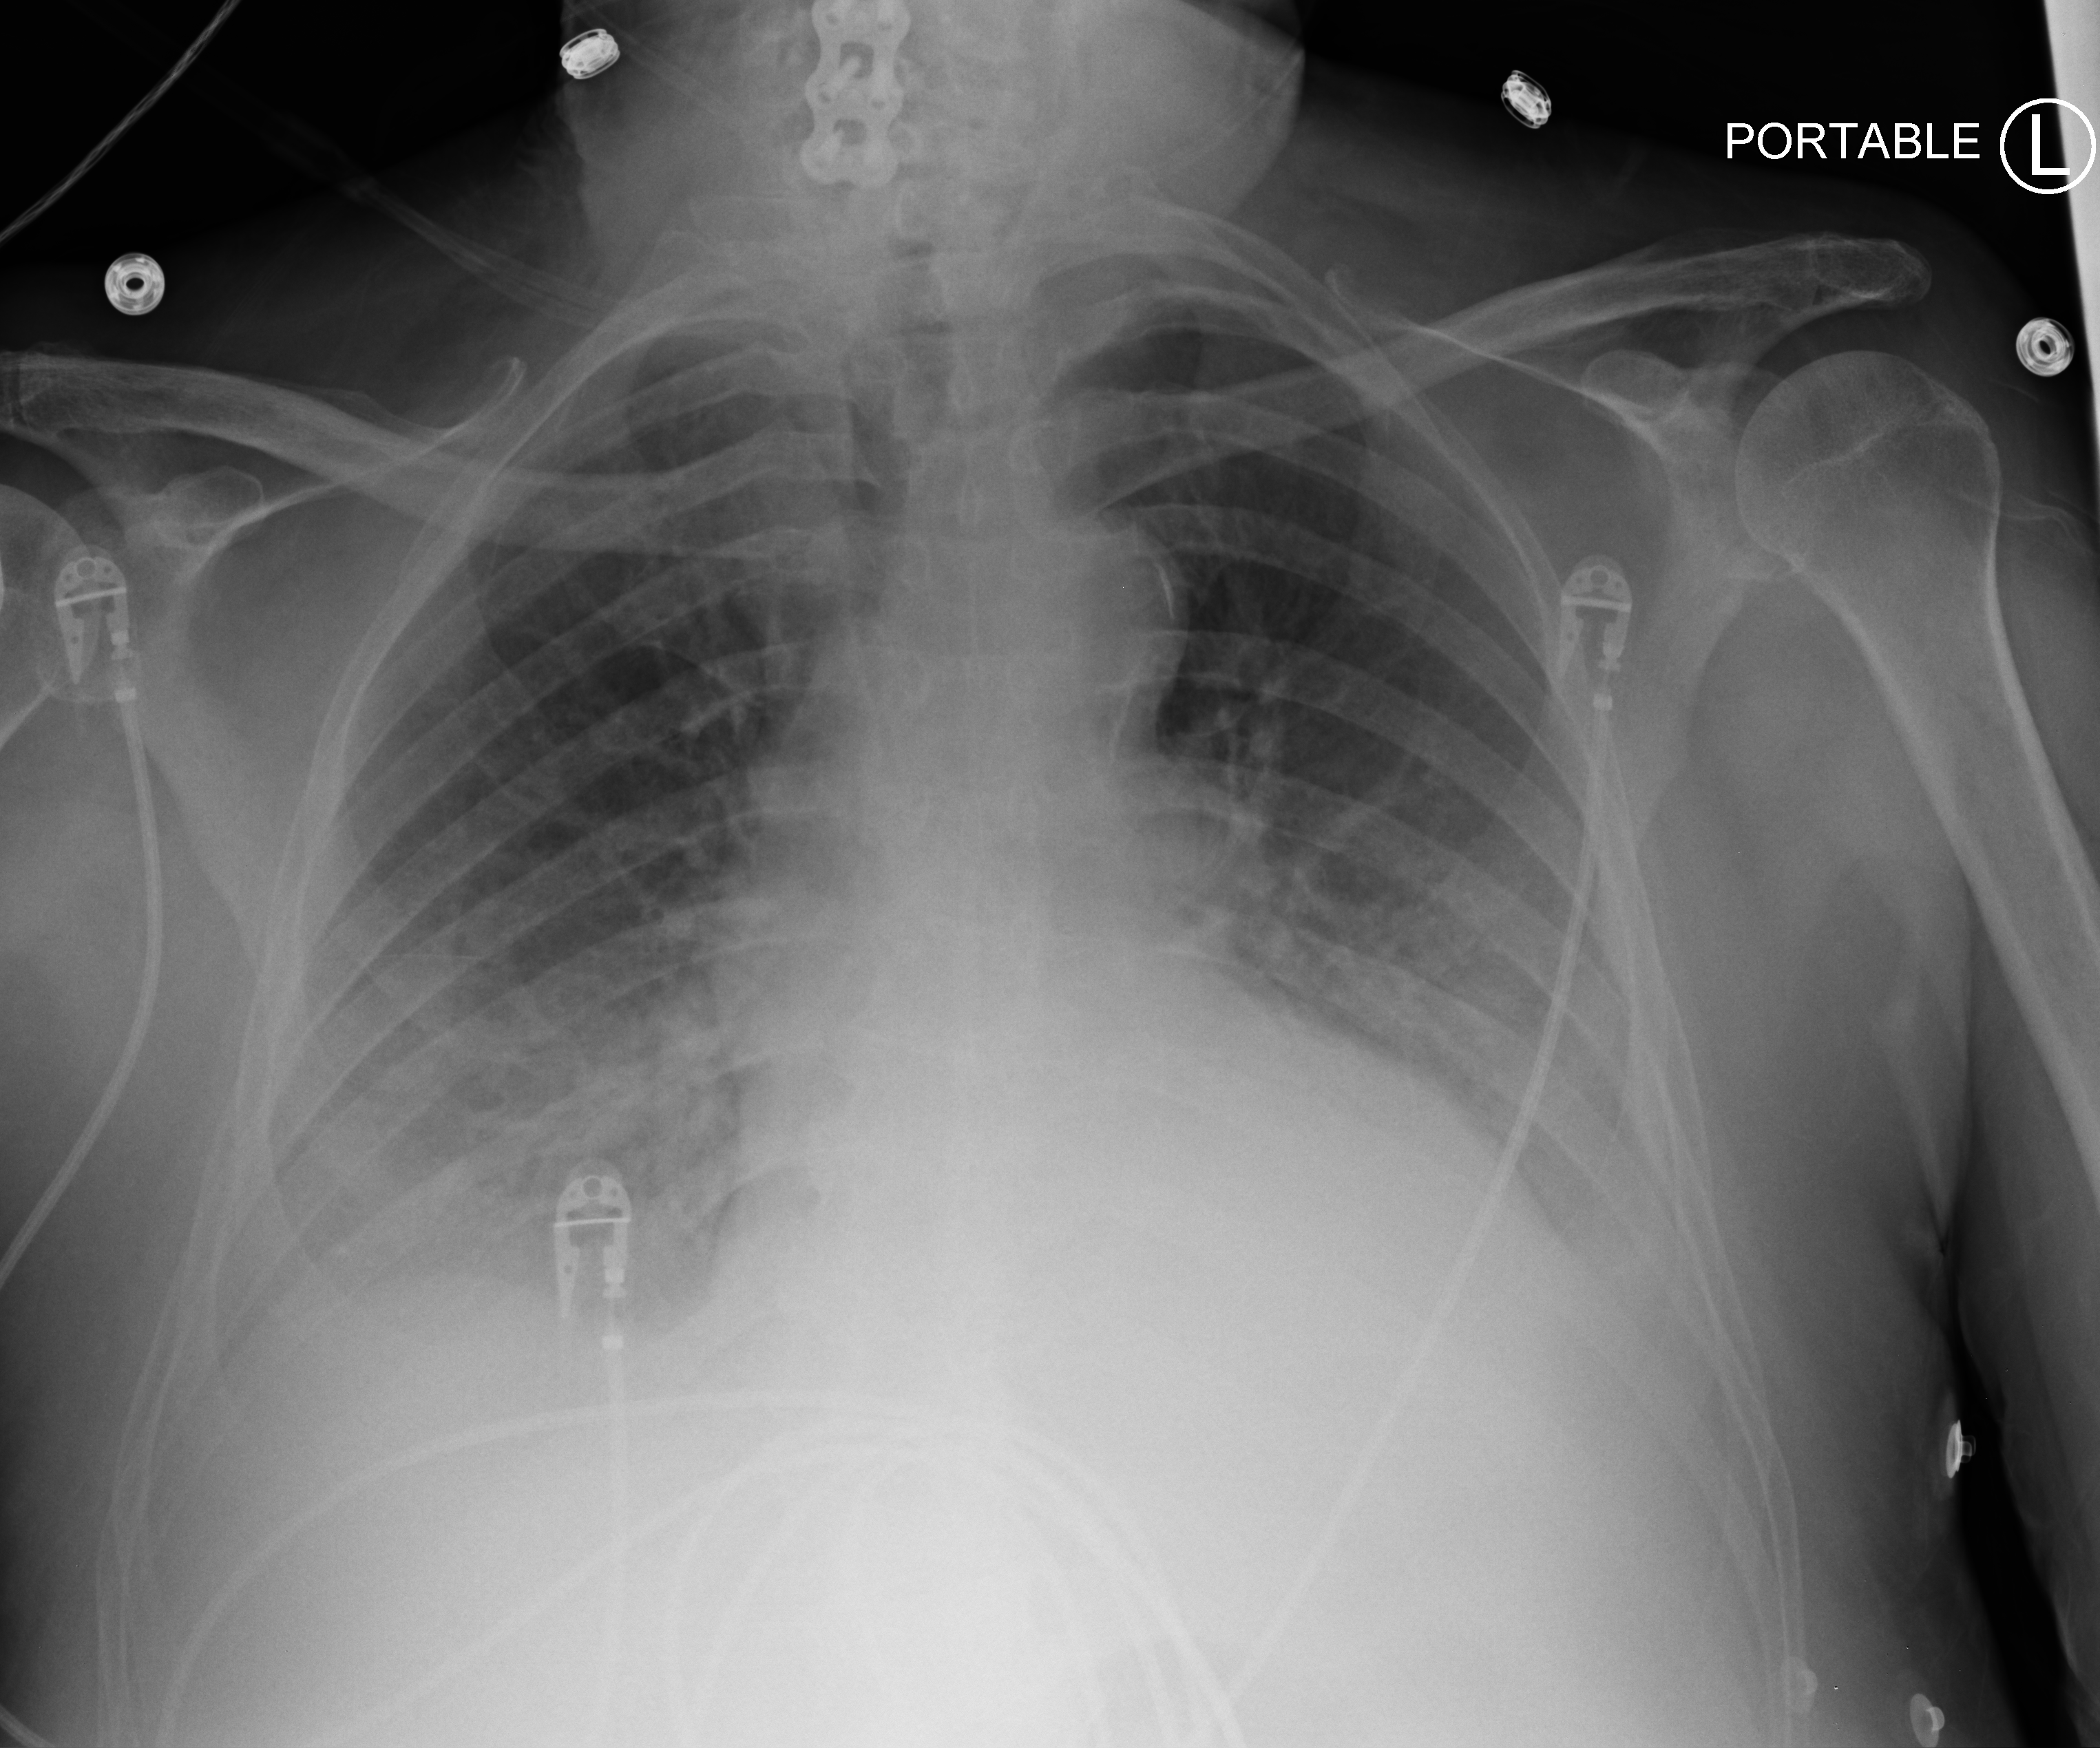
Chest X-ray (portable). Male patient hospitalised with COVID-19, age 75–90 years.
Admission-level facts for this patient (not findings on this image; timing relative to this image not recorded):
- admitted to intensive care during this hospital stay: yes